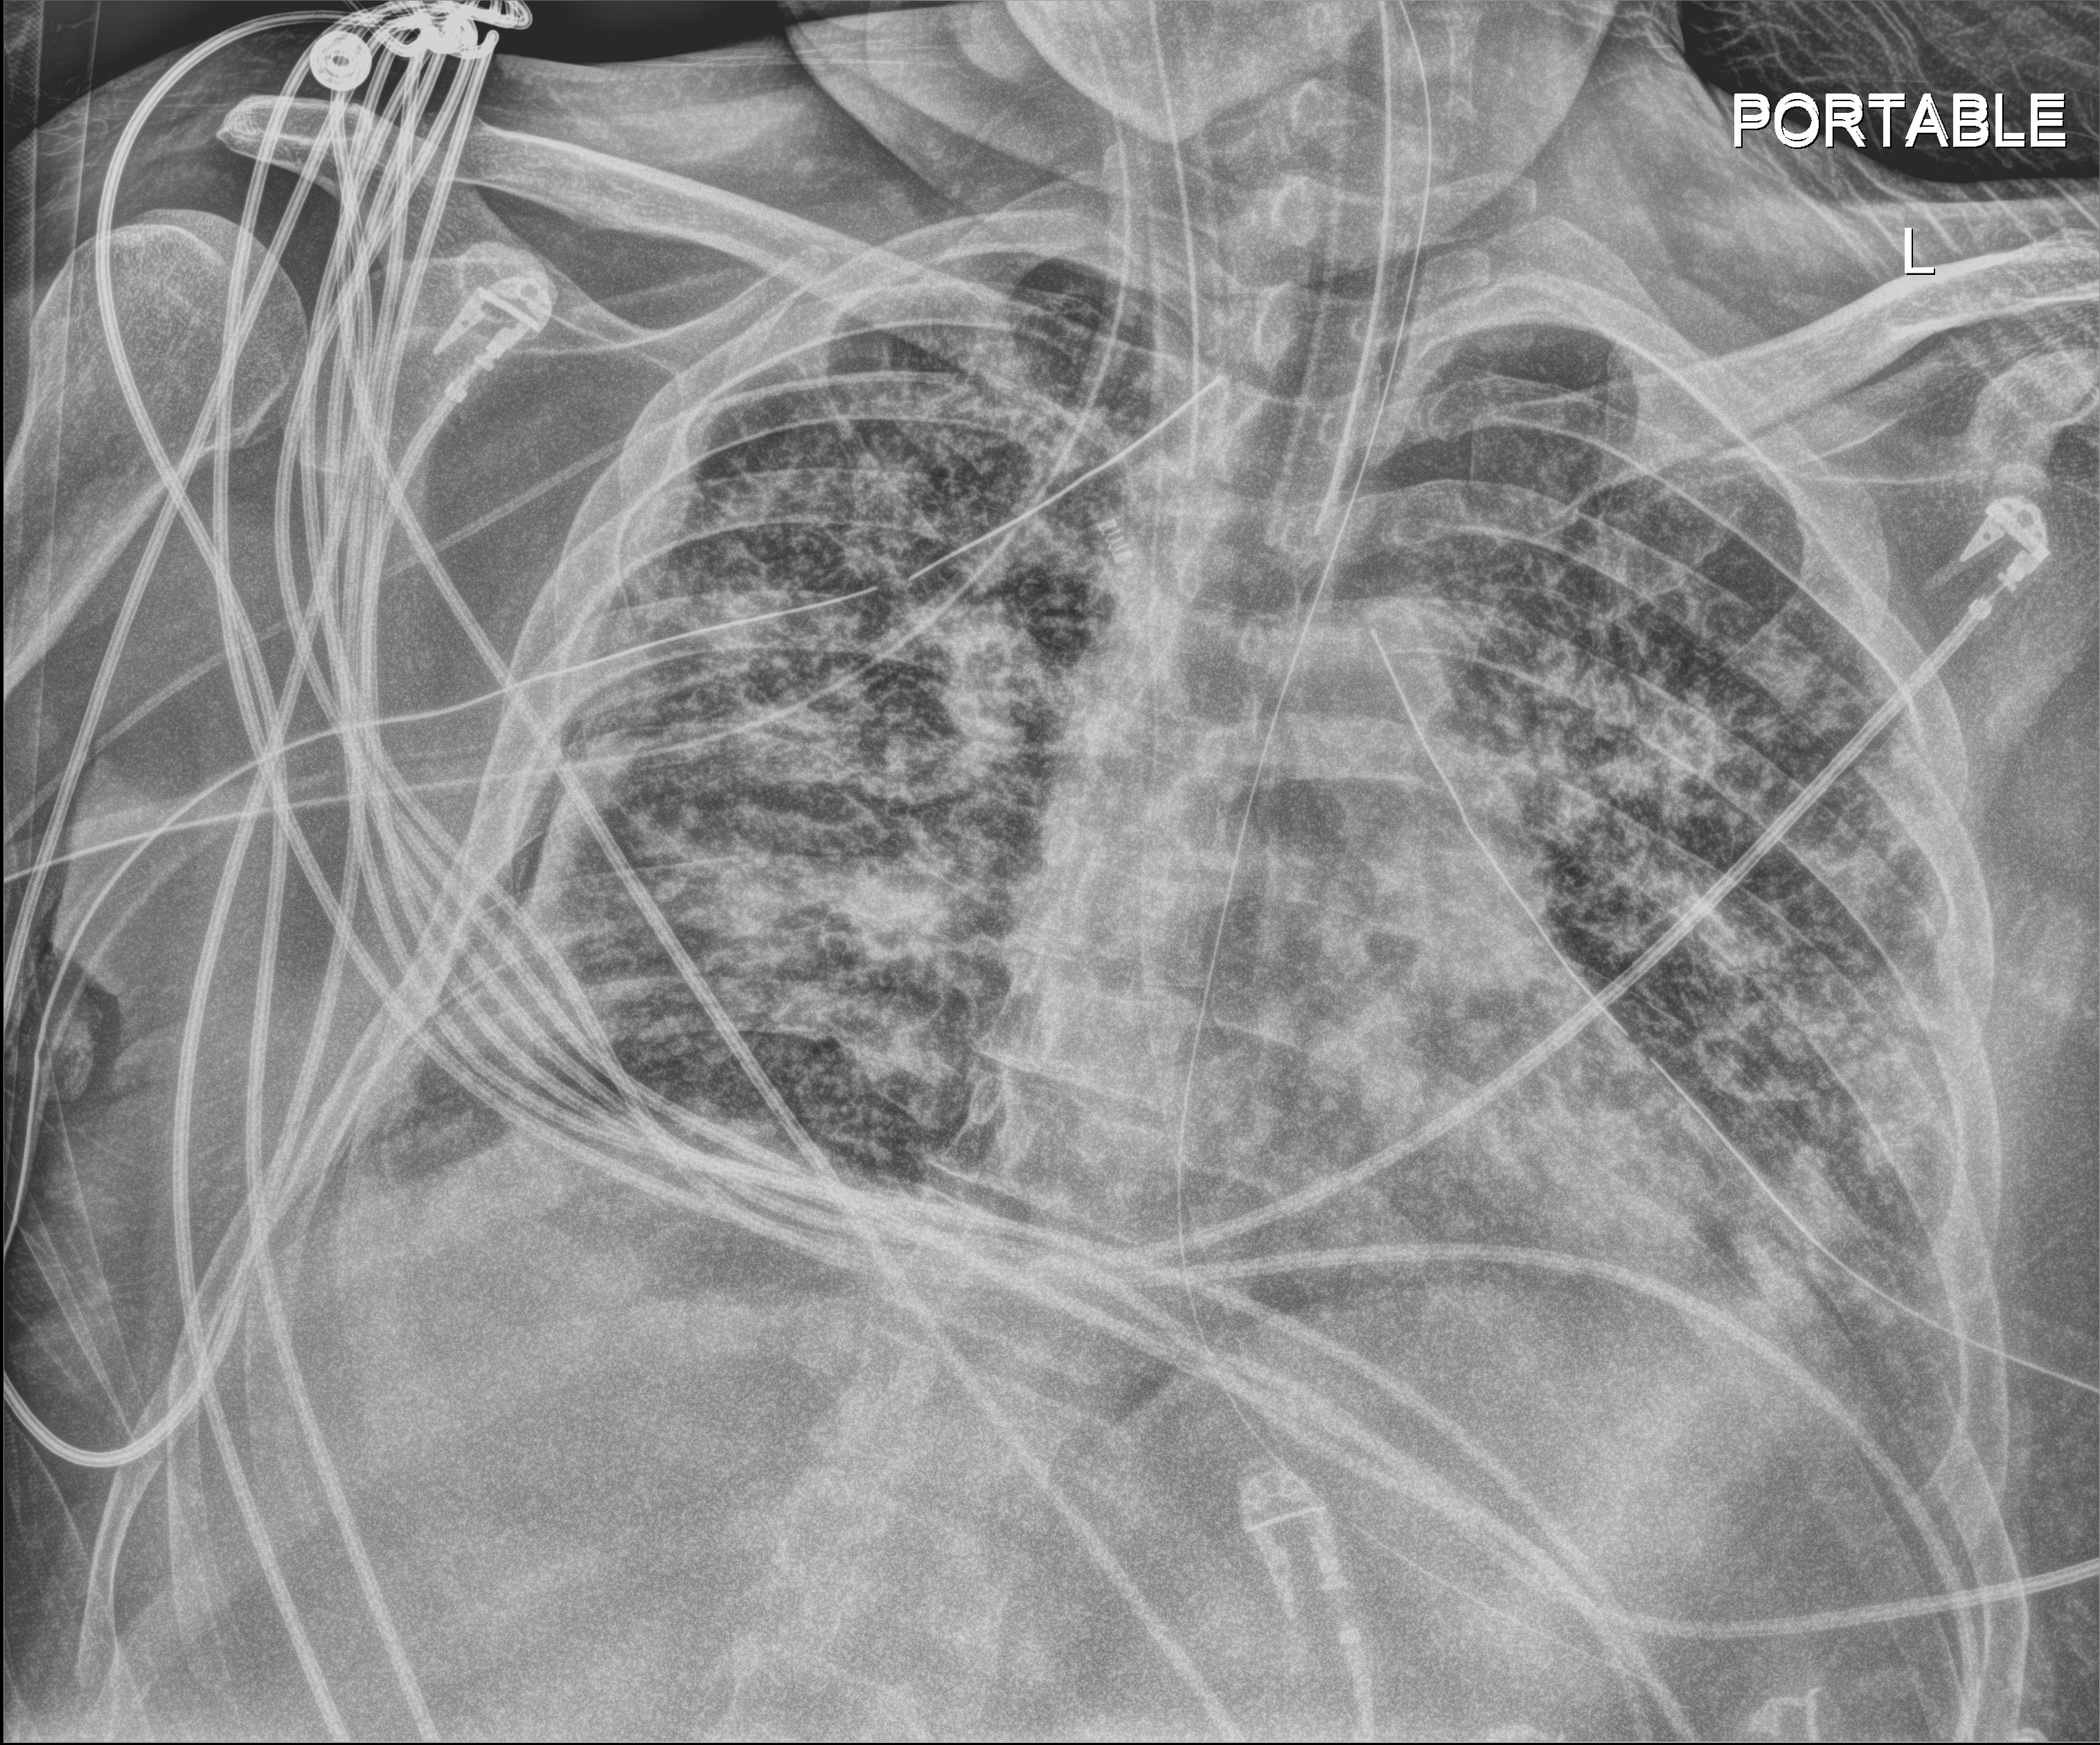
Chest X-ray (portable); anteroposterior (AP) projection. Male patient hospitalised with COVID-19, age 18–59 years.
From the hospital-stay record, not from the radiograph (when in the stay this image was taken is not recorded): mechanically ventilated during this hospital stay: yes; COPD (admission record): no; admitted to intensive care during this hospital stay: yes.